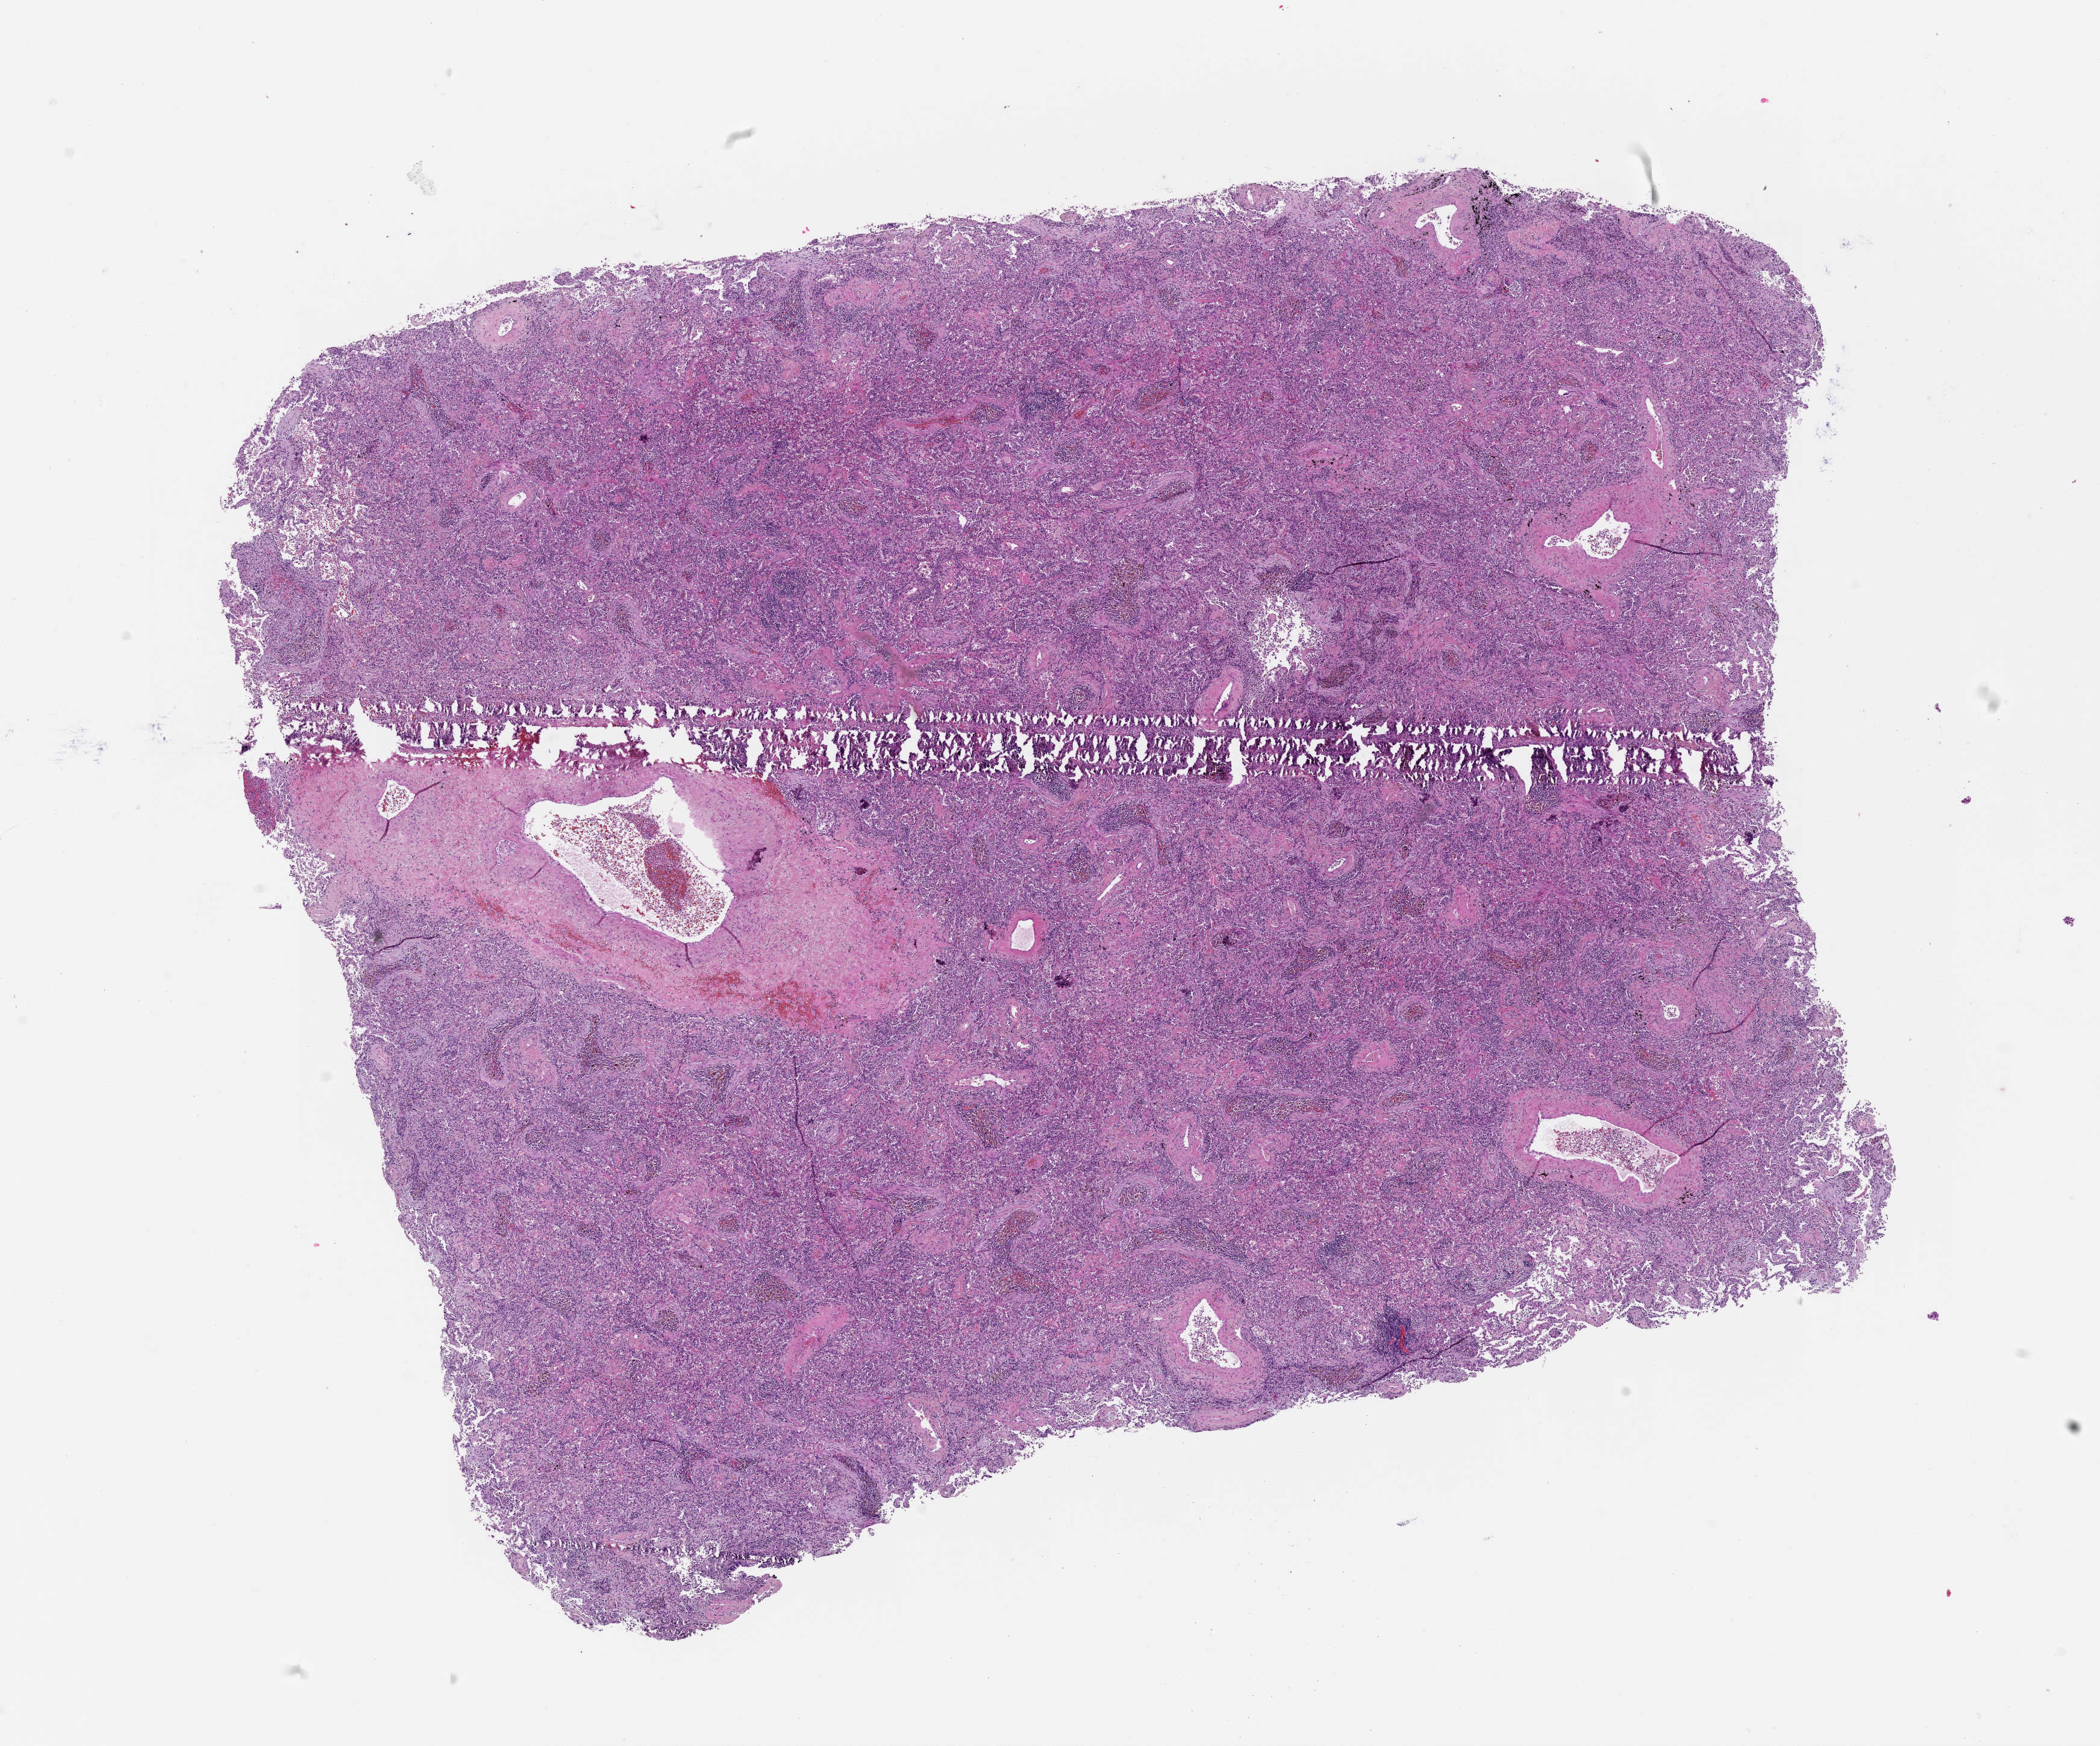
H&E whole-slide image — shown as a low-resolution overview of the whole scanned area (about 14.0 x 11.7 mm, from a 20x scan); lung, normal (non-tumour) tissue. 64-year-old male patient.
This section: normal (non-tumour) tissue from the same patient. Patient diagnosis (cohort enrolment): squamous cell carcinoma (lung).